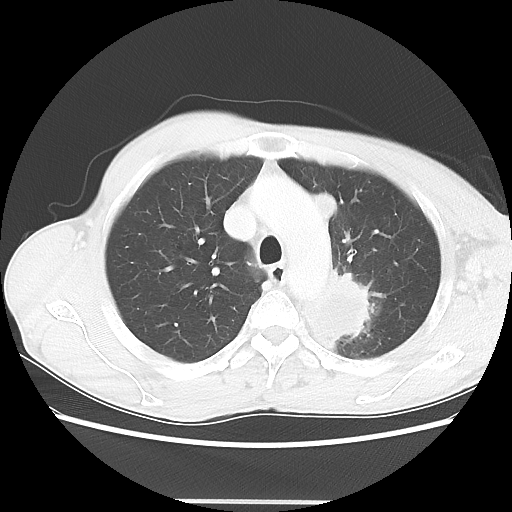
Chest CT, one axial slice; position 49 of 62 along the scan axis; lung window (W 1500 / L -600 HU); 5 mm slice thickness; 512 × 512 image matrix, field of view 360 × 360 mm. Male patient, age 61 years. Case-level facts recorded for this patient, not image findings: clinical TNM (as recorded): T3 N1 M1.
Annotated regions visible in this slice (rectangle marked by the reading radiologist):
- lung tumour (recorded histology: adenocarcinoma): bounding box <305,263,381,339> (left, top, right, bottom; pixels)
- lung tumour (recorded histology: adenocarcinoma): <310,189,344,224>